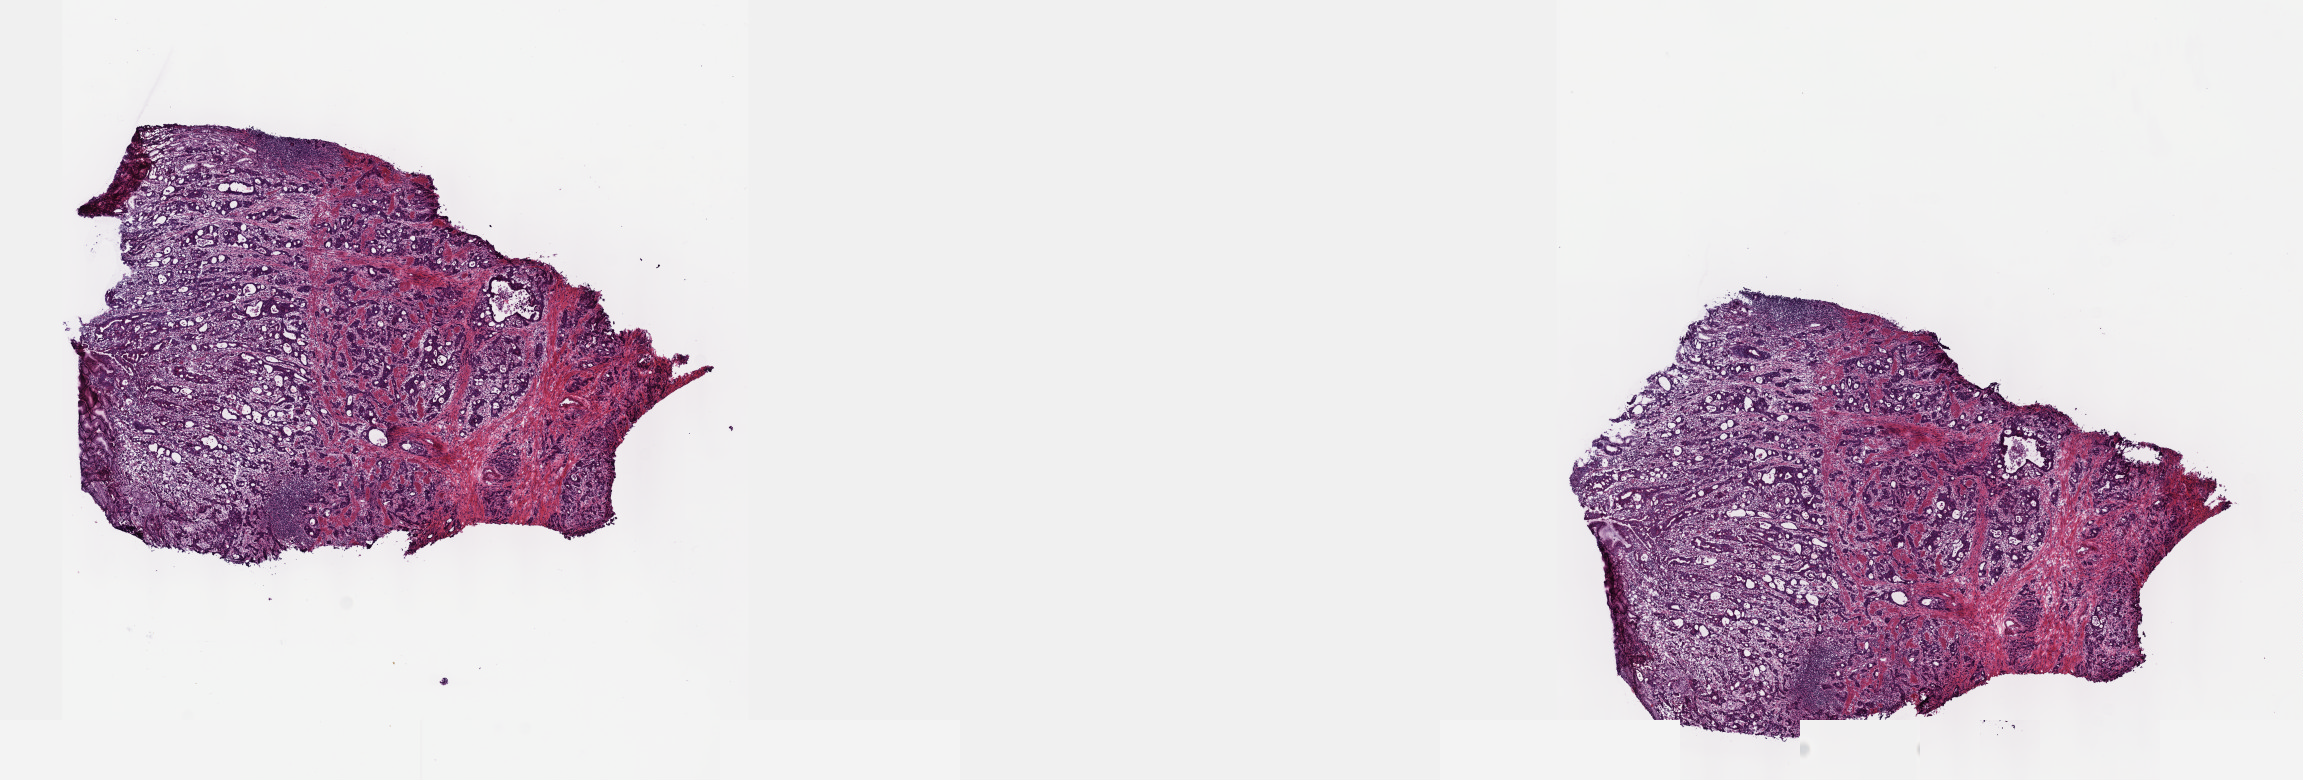
Digitized H&E tissue section (whole slide), shown as a low-resolution overview of the whole scanned area (about 18.6 x 6.3 mm). Frozen section. Sample: primary tumour, stomach. Female patient; age at initial diagnosis 47 years. Histologic grade: G2 (moderately differentiated). Slide review estimates, as recorded: tumour cells 100%, tumour nuclei 60%, normal cells 0%, stromal cells 0%, necrosis 0%. Inflammatory infiltration, as recorded: lymphocyte infiltration 5%, monocyte infiltration 0%, neutrophil infiltration 0%.
* TNM: T3 N2 M0
* histologic diagnosis: Tubular adenocarcinoma (gastric antrum)
* AJCC pathologic stage: IIIB
* lymph nodes positive (case pathology): 12 of 43 examined